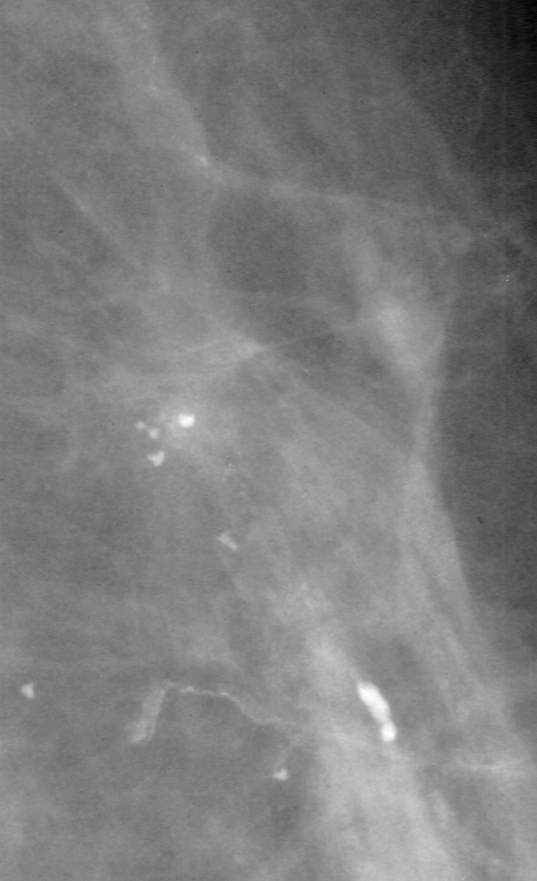
Cropped region of a digitized screen-film mammogram centred on a radiologist-marked abnormality, right breast, MLO view, BI-RADS breast density category 2 (scale 1–4).
Calcifications, morphology pleomorphic, distribution linear; BI-RADS assessment category 4; subtlety rating 2 on a 1 (subtle) to 5 (obvious) scale; pathology result (as recorded, not read from the image): malignant.